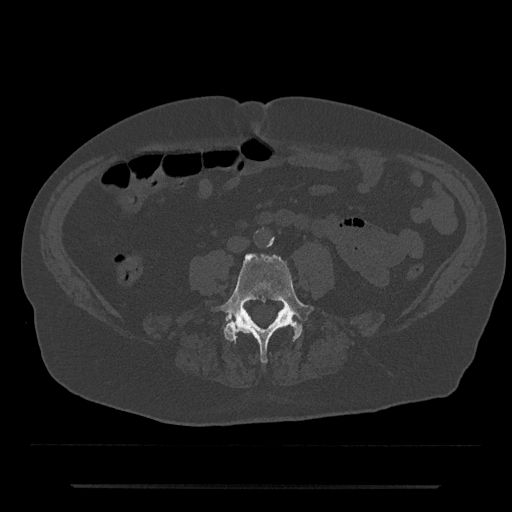
CT including the spine, one axial slice. Position 349 of 797 along the scan axis. Reconstruction kernel Br40s/3. 120 kVp. Bone window (W 1800 / L 400 HU). 0.5 mm slice thickness. 512 × 512 image matrix, field of view 434 × 434 mm. Patient: male, 80 years. From the clinical record (not read from this slice): primary cancer: prostate.
Outlined on this slice (semi-automatically segmented with operator editing):
- L4 vertebra: bounding box <217,253,315,363> (left, top, right, bottom; pixels)
- L5 vertebra: <229,320,301,336>